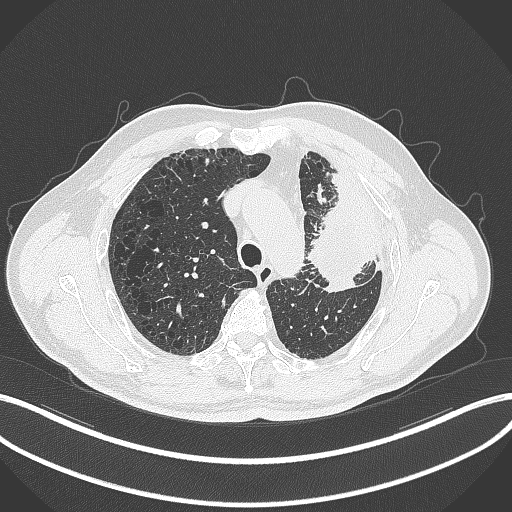
Chest CT, one axial slice; position 238 of 297 along the scan axis; reconstruction kernel B70f; lung window (W 1500 / L -600 HU); 512 × 512 image matrix, field of view 400 × 400 mm. Patient: male, 68 years. Case-level facts recorded for this patient, not image findings: clinical TNM (as recorded): T3 N3 M1.
Outlined on this slice (rectangle marked by the reading radiologist):
- lung tumour (recorded histology: adenocarcinoma): bounding box [x1, y1, x2, y2] px = [307, 190, 369, 297]